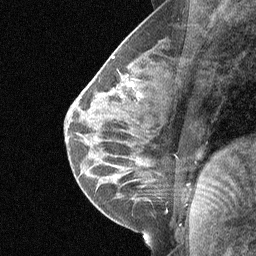
Breast MRI (dynamic contrast-enhanced), one sagittal slice. Slice 29 of 64 in the series (ordered by position). Dynamic contrast-enhanced study with each time point stored as its own series, time point 3 of 5 at this slice position (ordered by acquisition time). 1.5 T. TE 4.8 ms, TR 27 ms. 2 mm slice thickness. 256 × 256 image matrix, field of view 180 × 180 mm. Female patient, age 26 years. From the clinical record (not read from this slice): setting: breast cancer imaged before/during neoadjuvant chemotherapy; receptor status: HR-positive, HER2-negative.
Outlined on this slice (semi-automatically segmented with operator editing):
- analysis volume of interest (the breast-tissue region the enhancement analysis was run in; not a lesion): bounding box [x1, y1, x2, y2] px = [85, 46, 183, 144]
- tumour enhancement mask (voxels above the 90 % enhancement threshold inside the analysis volume of interest): [129, 83, 132, 85]